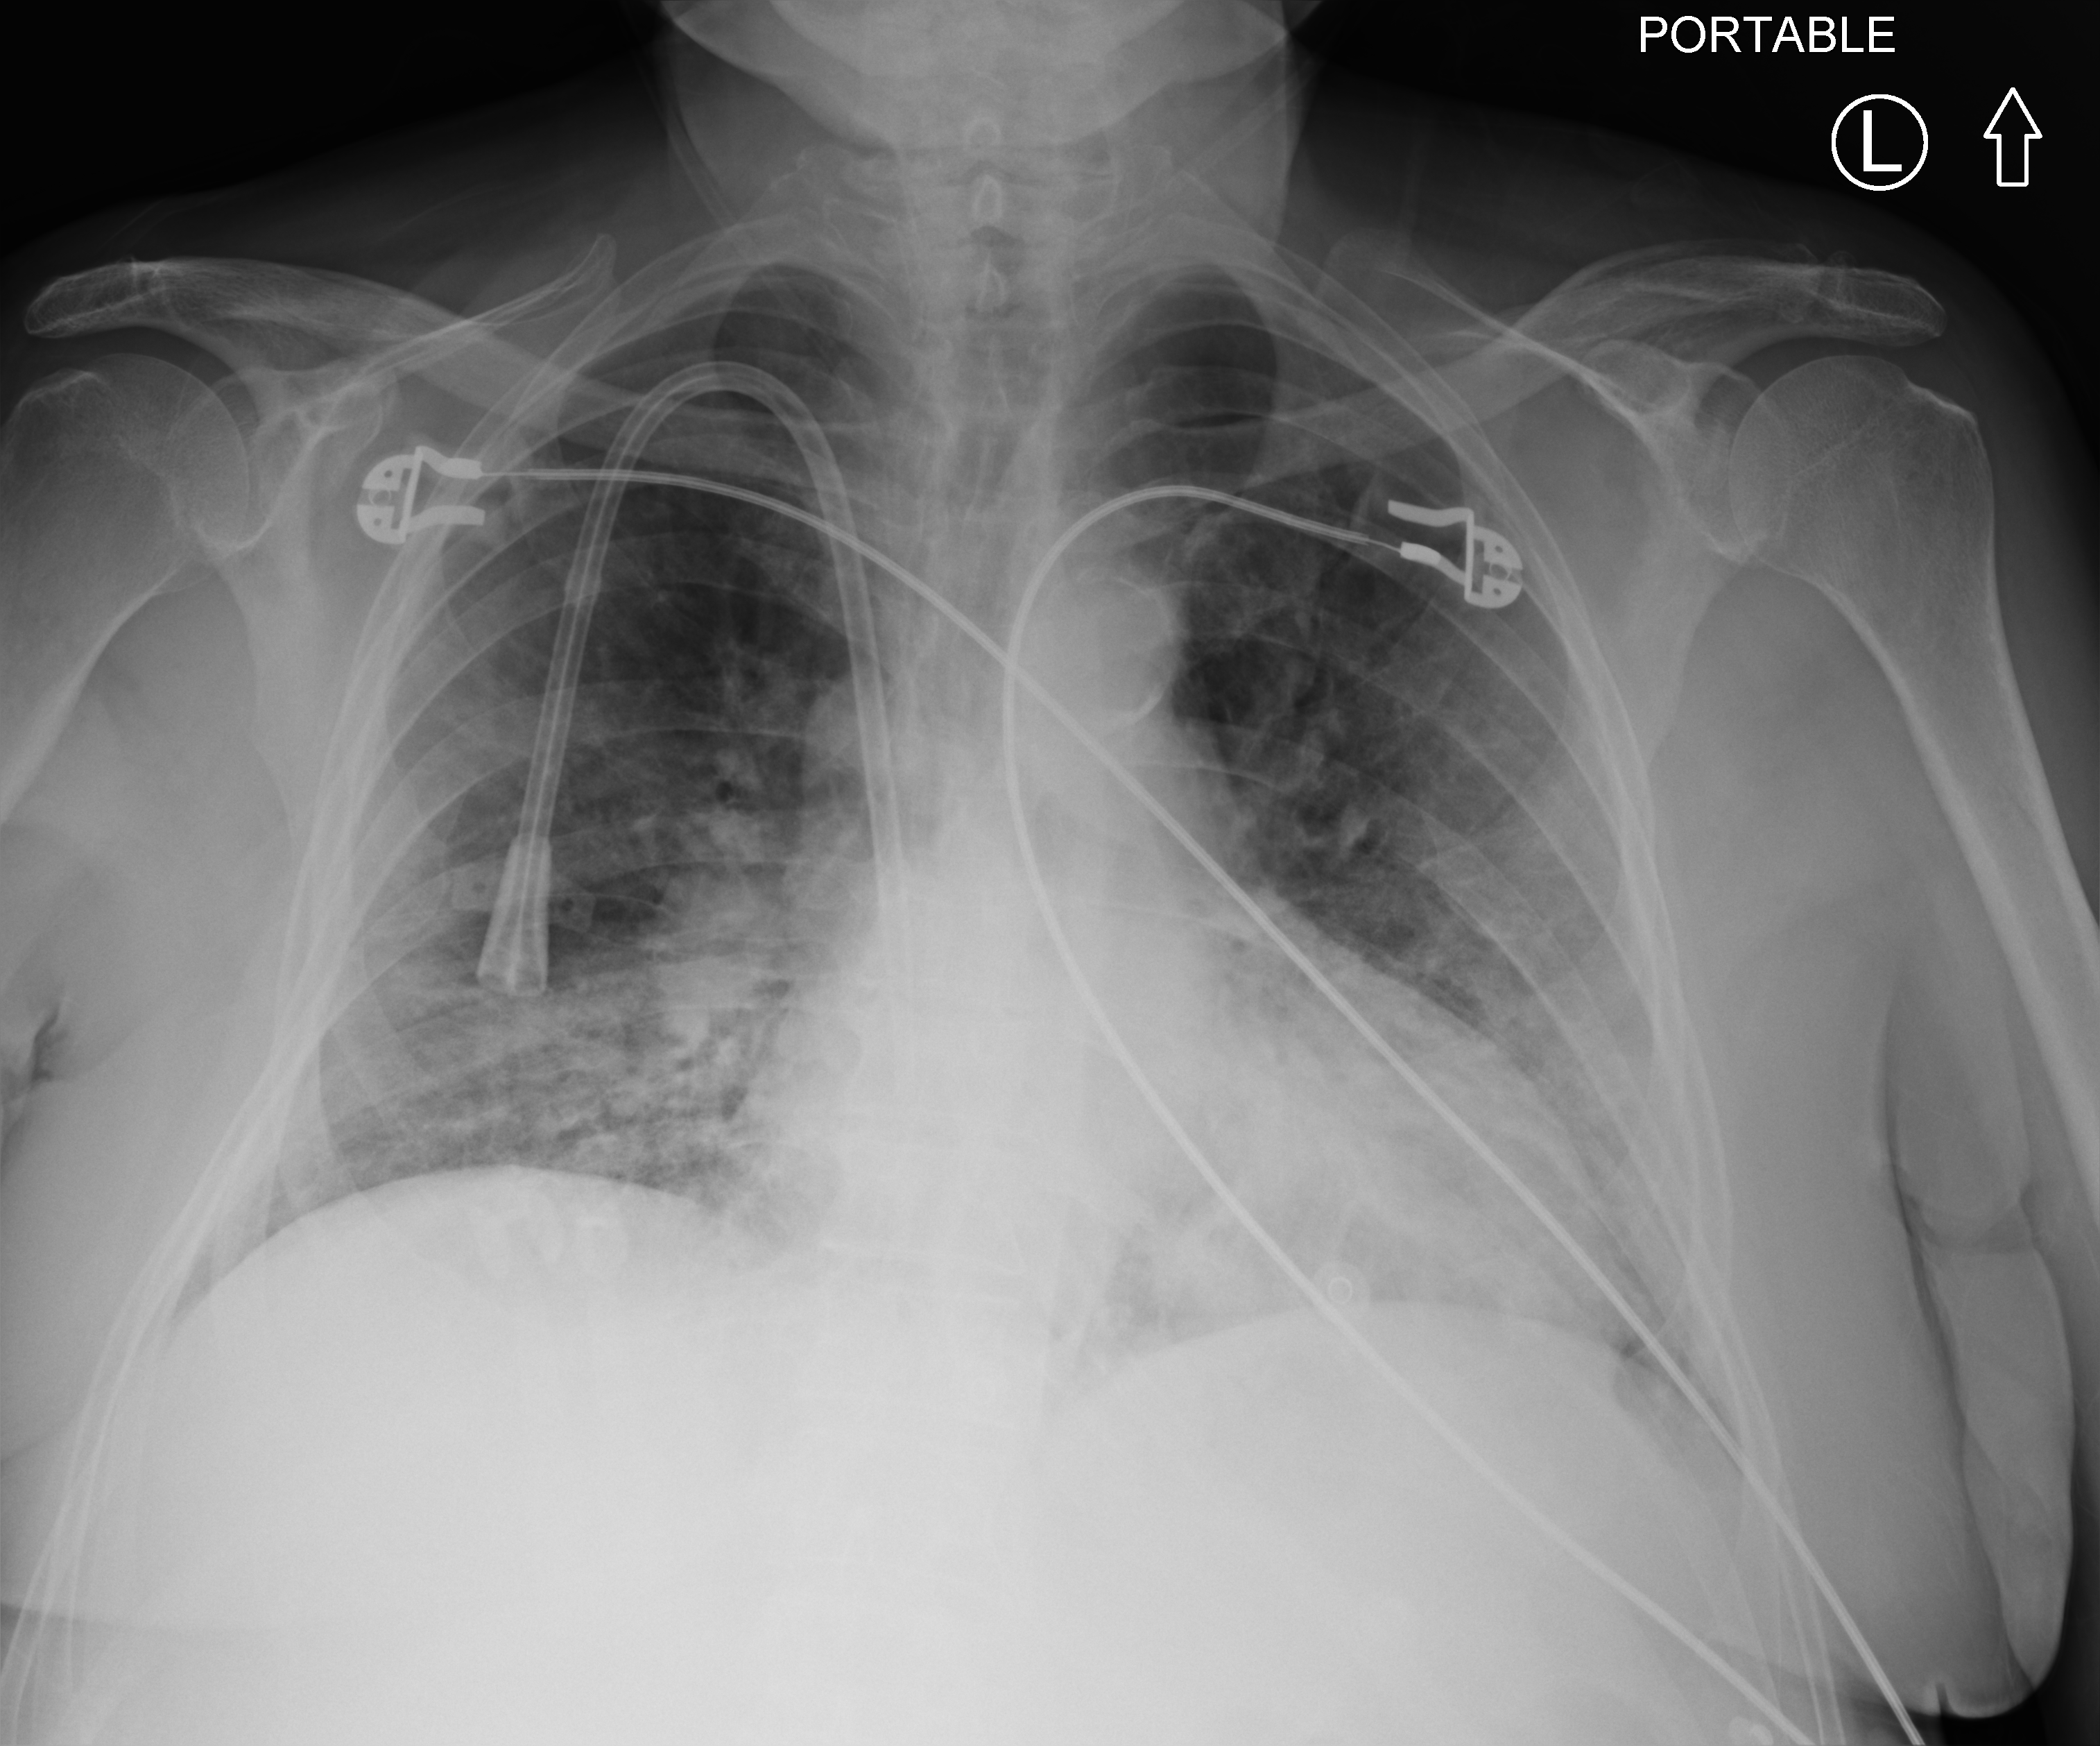
Bedside chest radiograph (computed radiography); anteroposterior (AP) projection. Male patient hospitalised with COVID-19, age 60–74 years.
From the hospital-stay record, not from the radiograph (when in the stay this image was taken is not recorded): length of hospital stay: 14 days.